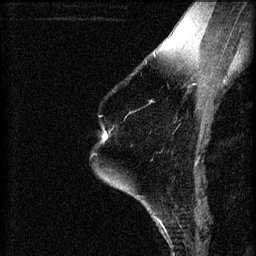
Breast MRI (dynamic contrast-enhanced), one sagittal slice. Slice 46 of 60 in the series (ordered by position). 3 images stored at this slice position (order not interpretable as contrast timing). 1.5 T. TE 4.2 ms, TR 8.2 ms. 2 mm slice thickness. 256 × 256 image matrix. Patient: female, 60 years.
Annotated regions visible in this slice (semi-automatic segmentation, software-assisted and operator-edited):
- analysis volume of interest (the breast-tissue region the enhancement analysis was run in; not a lesion): box from (x=100, y=126) to (x=111, y=145) px
- tumour enhancement mask (voxels above the 70 % enhancement threshold inside the analysis volume of interest): (x=102, y=134)–(x=108, y=139)